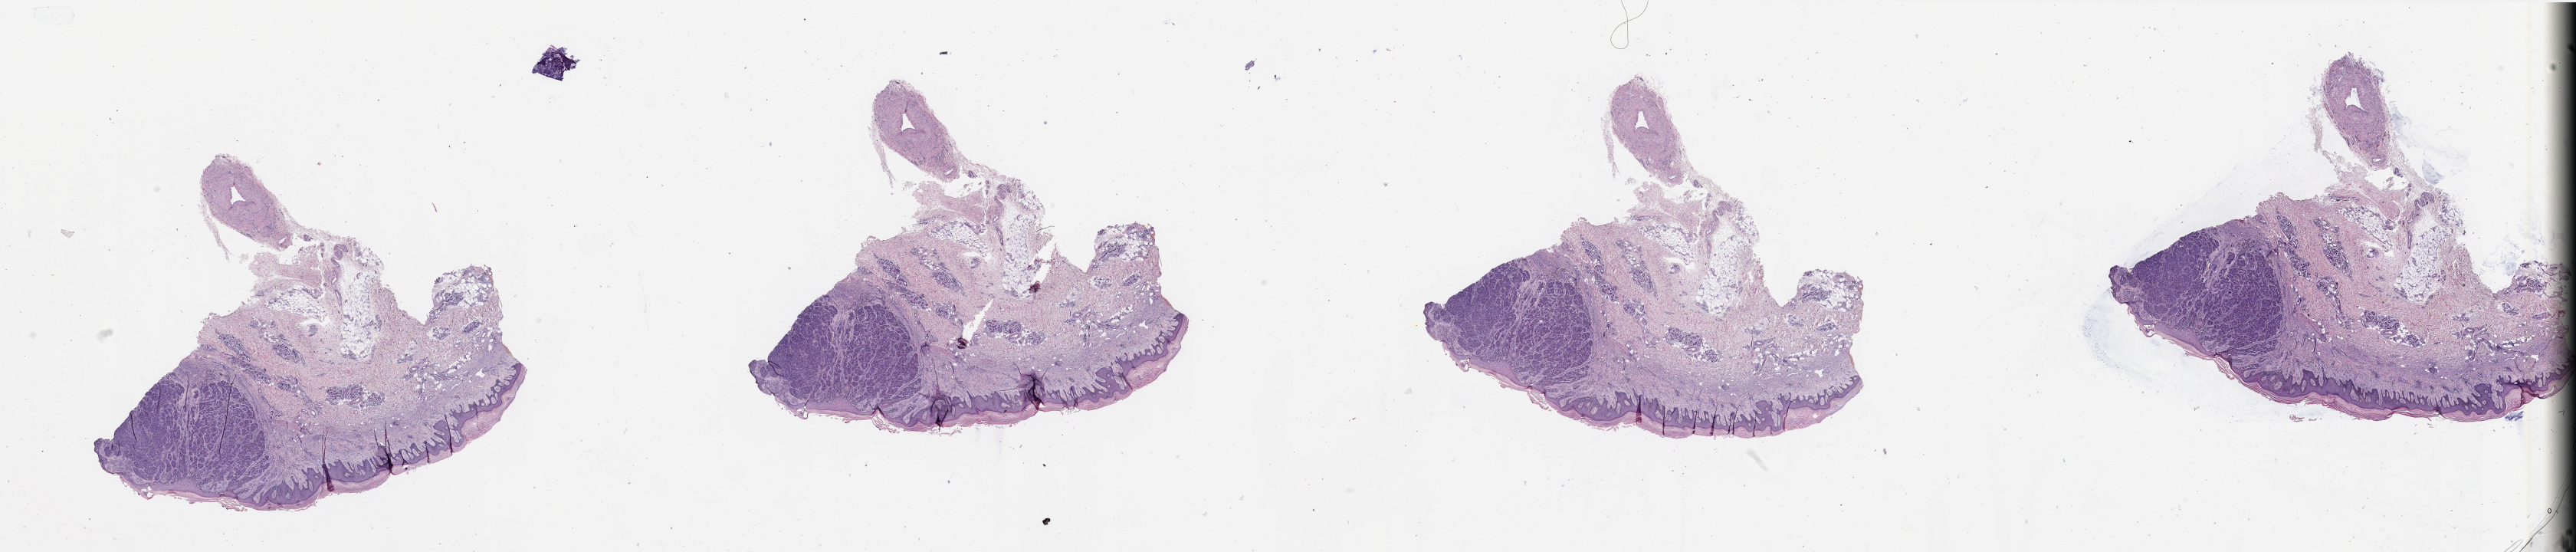
Hematoxylin and eosin (H&E) stained whole-slide image — a low-resolution overview of the entire scanned area, about 53.2 x 11.4 mm; melanoma tumour tissue; sampled site not recorded. Patient: female, aged 90 or older.
Diagnosis: Malignant melanoma, NOS. AJCC pathologic stage: IIC. Primary tumour site (as recorded): extremities.